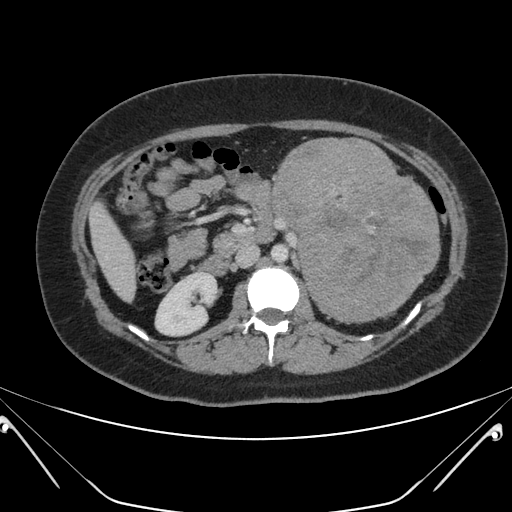
Contrast-enhanced abdominal CT, one axial slice. Intravenous contrast given. Soft-tissue window (W 400 / L 40 HU). 3 mm slice thickness. 512 × 512 image matrix. Patient: female, 26 years. From the clinical record (not read from this slice): diagnosis: adrenocortical carcinoma; tumour side: left adrenal; tumour size at pathology: 28 cm; Ki-67 index: 20 %; stage (as recorded): 2.
Structures marked on this image (semi-automatic segmentation, software-assisted and operator-edited):
- mass: bounding box [x1, y1, x2, y2] px = [274, 137, 440, 321]